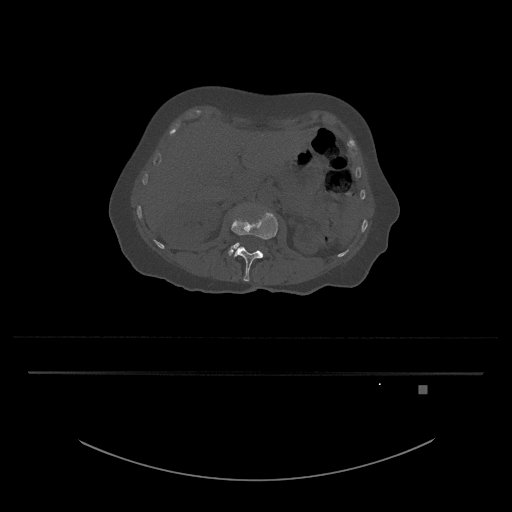
CT including the spine, one axial slice; slice 477 of 797 in the series (ordered by position); reconstruction kernel Br40s/3; 120 kVp; bone window (W 1800 / L 400 HU); 0.5 mm slice thickness; 512 × 512 image matrix, field of view 500 × 500 mm. Patient: female, 57 years. From the clinical record (not read from this slice): primary cancer: cervical.
Structures marked on this image (semi-automatically segmented with operator editing):
- L3 vertebra: bounding box (x1, y1, x2, y2) in pixels: (228, 242, 241, 255)